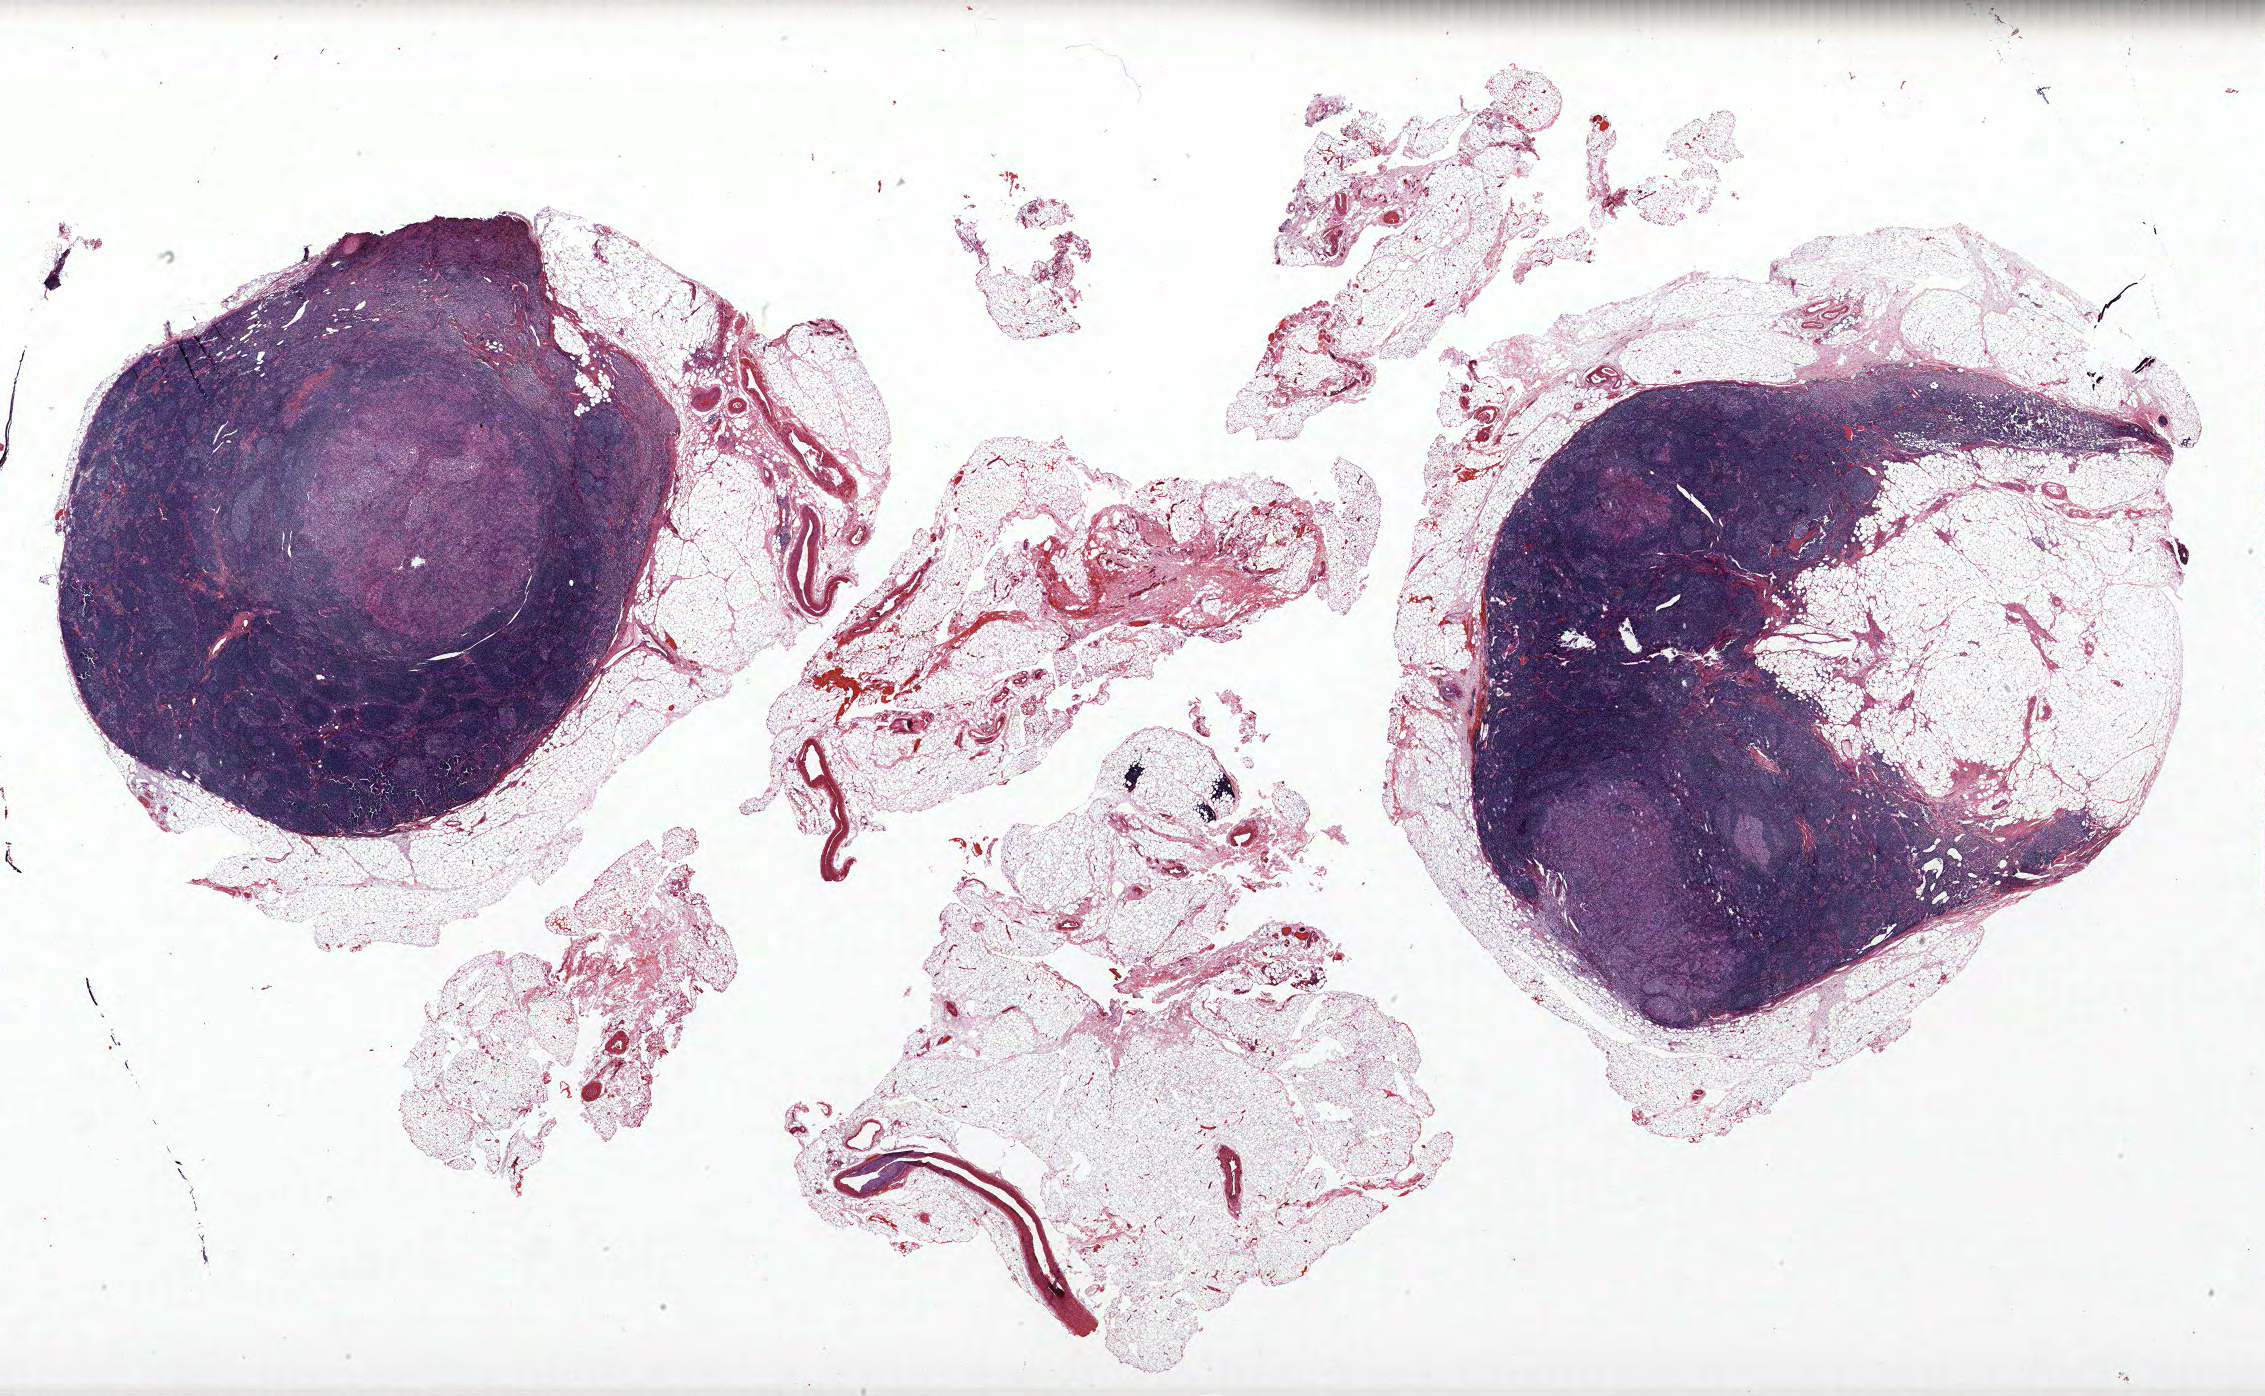
Hematoxylin and eosin (H&E) stained whole-slide image, a low-resolution overview of the entire scanned area, about 36.2 x 22.3 mm (from a 40x scan), formalin-fixed paraffin-embedded (FFPE) section, lung tissue. Male, age 70 at enrolment. Former smoker at enrolment.
Participant's lung-cancer diagnosis: Adenocarcinoma, NOS (ICD-O-3 8140/3).